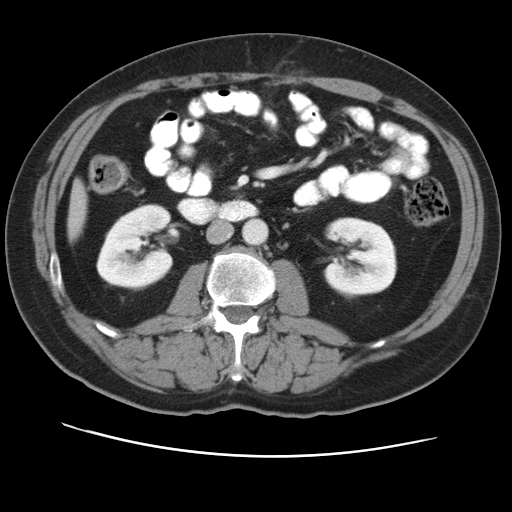
Contrast-enhanced abdominal CT, one axial slice; intravenous contrast given; soft-tissue window (W 400 / L 40 HU); 5 mm slice thickness; 512 × 512 image matrix. Male patient, age 59 years. From the clinical record (not read from this slice): diagnosis: colorectal cancer liver metastases, imaged before liver resection; multiple liver metastases: yes.
Outlined on this slice (expert manual segmentation):
- liver: bounding box <71,198,80,234> (left, top, right, bottom; pixels)